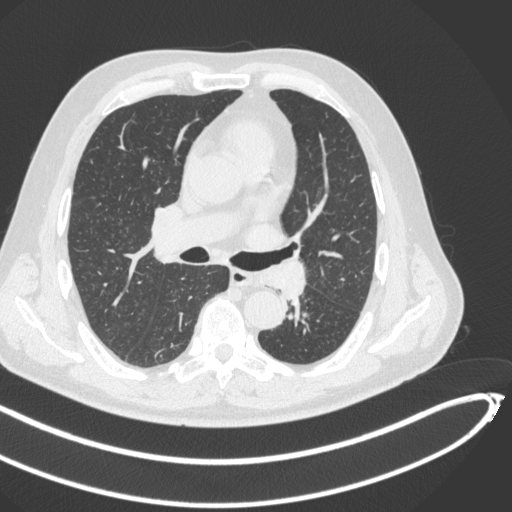
Chest CT, one axial slice. Position 269 of 466 along the scan axis. 120 kVp. Lung window (W 1500 / L -600 HU). 1 mm slice thickness. 512 × 512 image matrix, field of view 400 × 400 mm. Patient: male, 64 years. Case-level facts recorded for this patient, not image findings: clinical TNM (as recorded): T1c N0 M0.
Structures marked on this image (rectangle marked by the reading radiologist):
- lung tumour (recorded histology: squamous cell carcinoma): box from (x=255, y=261) to (x=310, y=304) px